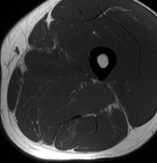
MRI of an extremity soft-tissue mass, one axial slice. Slice 38 of 70 in the series (ordered by position). MR volume resampled by the dataset authors to the PET/CT grid (not the native acquisition matrix). 157 × 163 image matrix, field of view 153 × 159 mm. Male patient. From the clinical record (not read from this slice): histological type: extraskeletal osteosarcoma; grade: high; site of the primary tumour: left adductur.
Structures marked on this image (expert contour drawn on MRI and transferred to this co-registered scan by the dataset authors):
- gross tumour volume (mass): box from (x=17, y=69) to (x=123, y=121) px